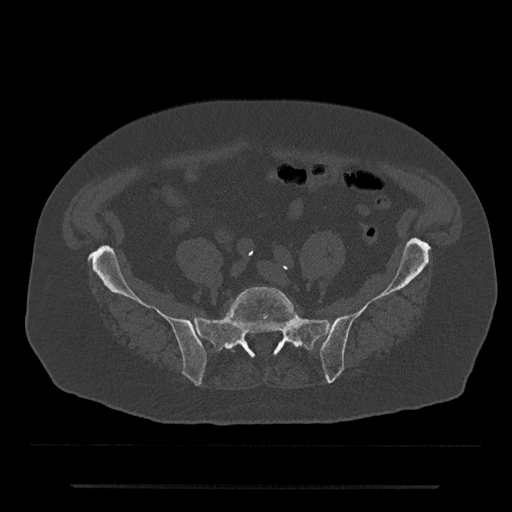
CT including the spine, one axial slice; position 253 of 797 along the scan axis; 120 kVp; bone window (W 1800 / L 400 HU); 0.5 mm slice thickness; 512 × 512 image matrix, field of view 434 × 434 mm. Patient: male, 80 years. From the clinical record (not read from this slice): primary cancer: prostate; vertebrae with lytic lesions (as recorded): L1, T11.
Annotated regions visible in this slice (semi-automatically segmented with operator editing):
- L5 vertebra: box from (x=226, y=287) to (x=297, y=351) px